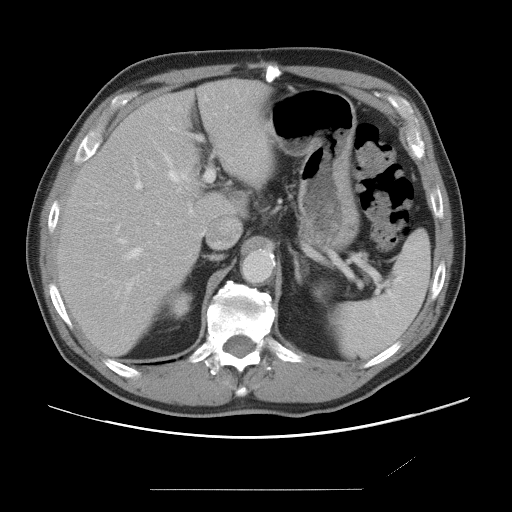
Contrast-enhanced abdominal CT, one axial slice. Position 48 of 87 along the scan axis. Intravenous contrast given. Soft-tissue window (W 400 / L 40 HU). 512 × 512 image matrix, field of view 406 × 406 mm. Male patient, age 74 years. Case-level facts recorded for this patient, not image findings: diagnosis: colorectal cancer liver metastases, imaged before liver resection; multiple liver metastases: yes; largest metastasis: 1.1 cm; chemotherapy before resection: yes.
Annotated regions visible in this slice (outlined manually by an expert reader):
- hepatic veins: bounding box [x1, y1, x2, y2] px = [119, 154, 187, 258]
- liver: [59, 79, 274, 355]
- planned liver remnant (the part of the liver to remain after resection): [59, 79, 275, 355]
- portal vein (with intrahepatic branches): [116, 137, 214, 293]